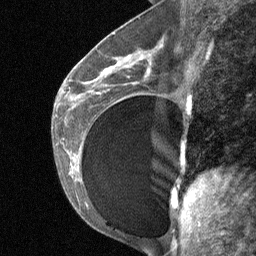
Breast MRI (dynamic contrast-enhanced), one sagittal slice. Slice 36 of 64 in the series (ordered by position). Dynamic contrast-enhanced study with each time point stored as its own series, time point 2 of 3 at this slice position (early post-contrast, ordered by acquisition time). 1.5 T. TE 4.8 ms, TR 27 ms. 2 mm slice thickness. 256 × 256 image matrix, field of view 180 × 180 mm. Patient: female, 35 years. From the clinical record (not read from this slice): setting: breast cancer imaged before/during neoadjuvant chemotherapy; receptor status: HR-positive, HER2-negative.
Annotated regions visible in this slice (semi-automatic segmentation, software-assisted and operator-edited):
- analysis volume of interest (the breast-tissue region the enhancement analysis was run in; not a lesion): bounding box (x1, y1, x2, y2) in pixels: (74, 58, 162, 171)
- tumour enhancement mask (voxels above the 90 % enhancement threshold inside the analysis volume of interest): (104, 69, 109, 73)